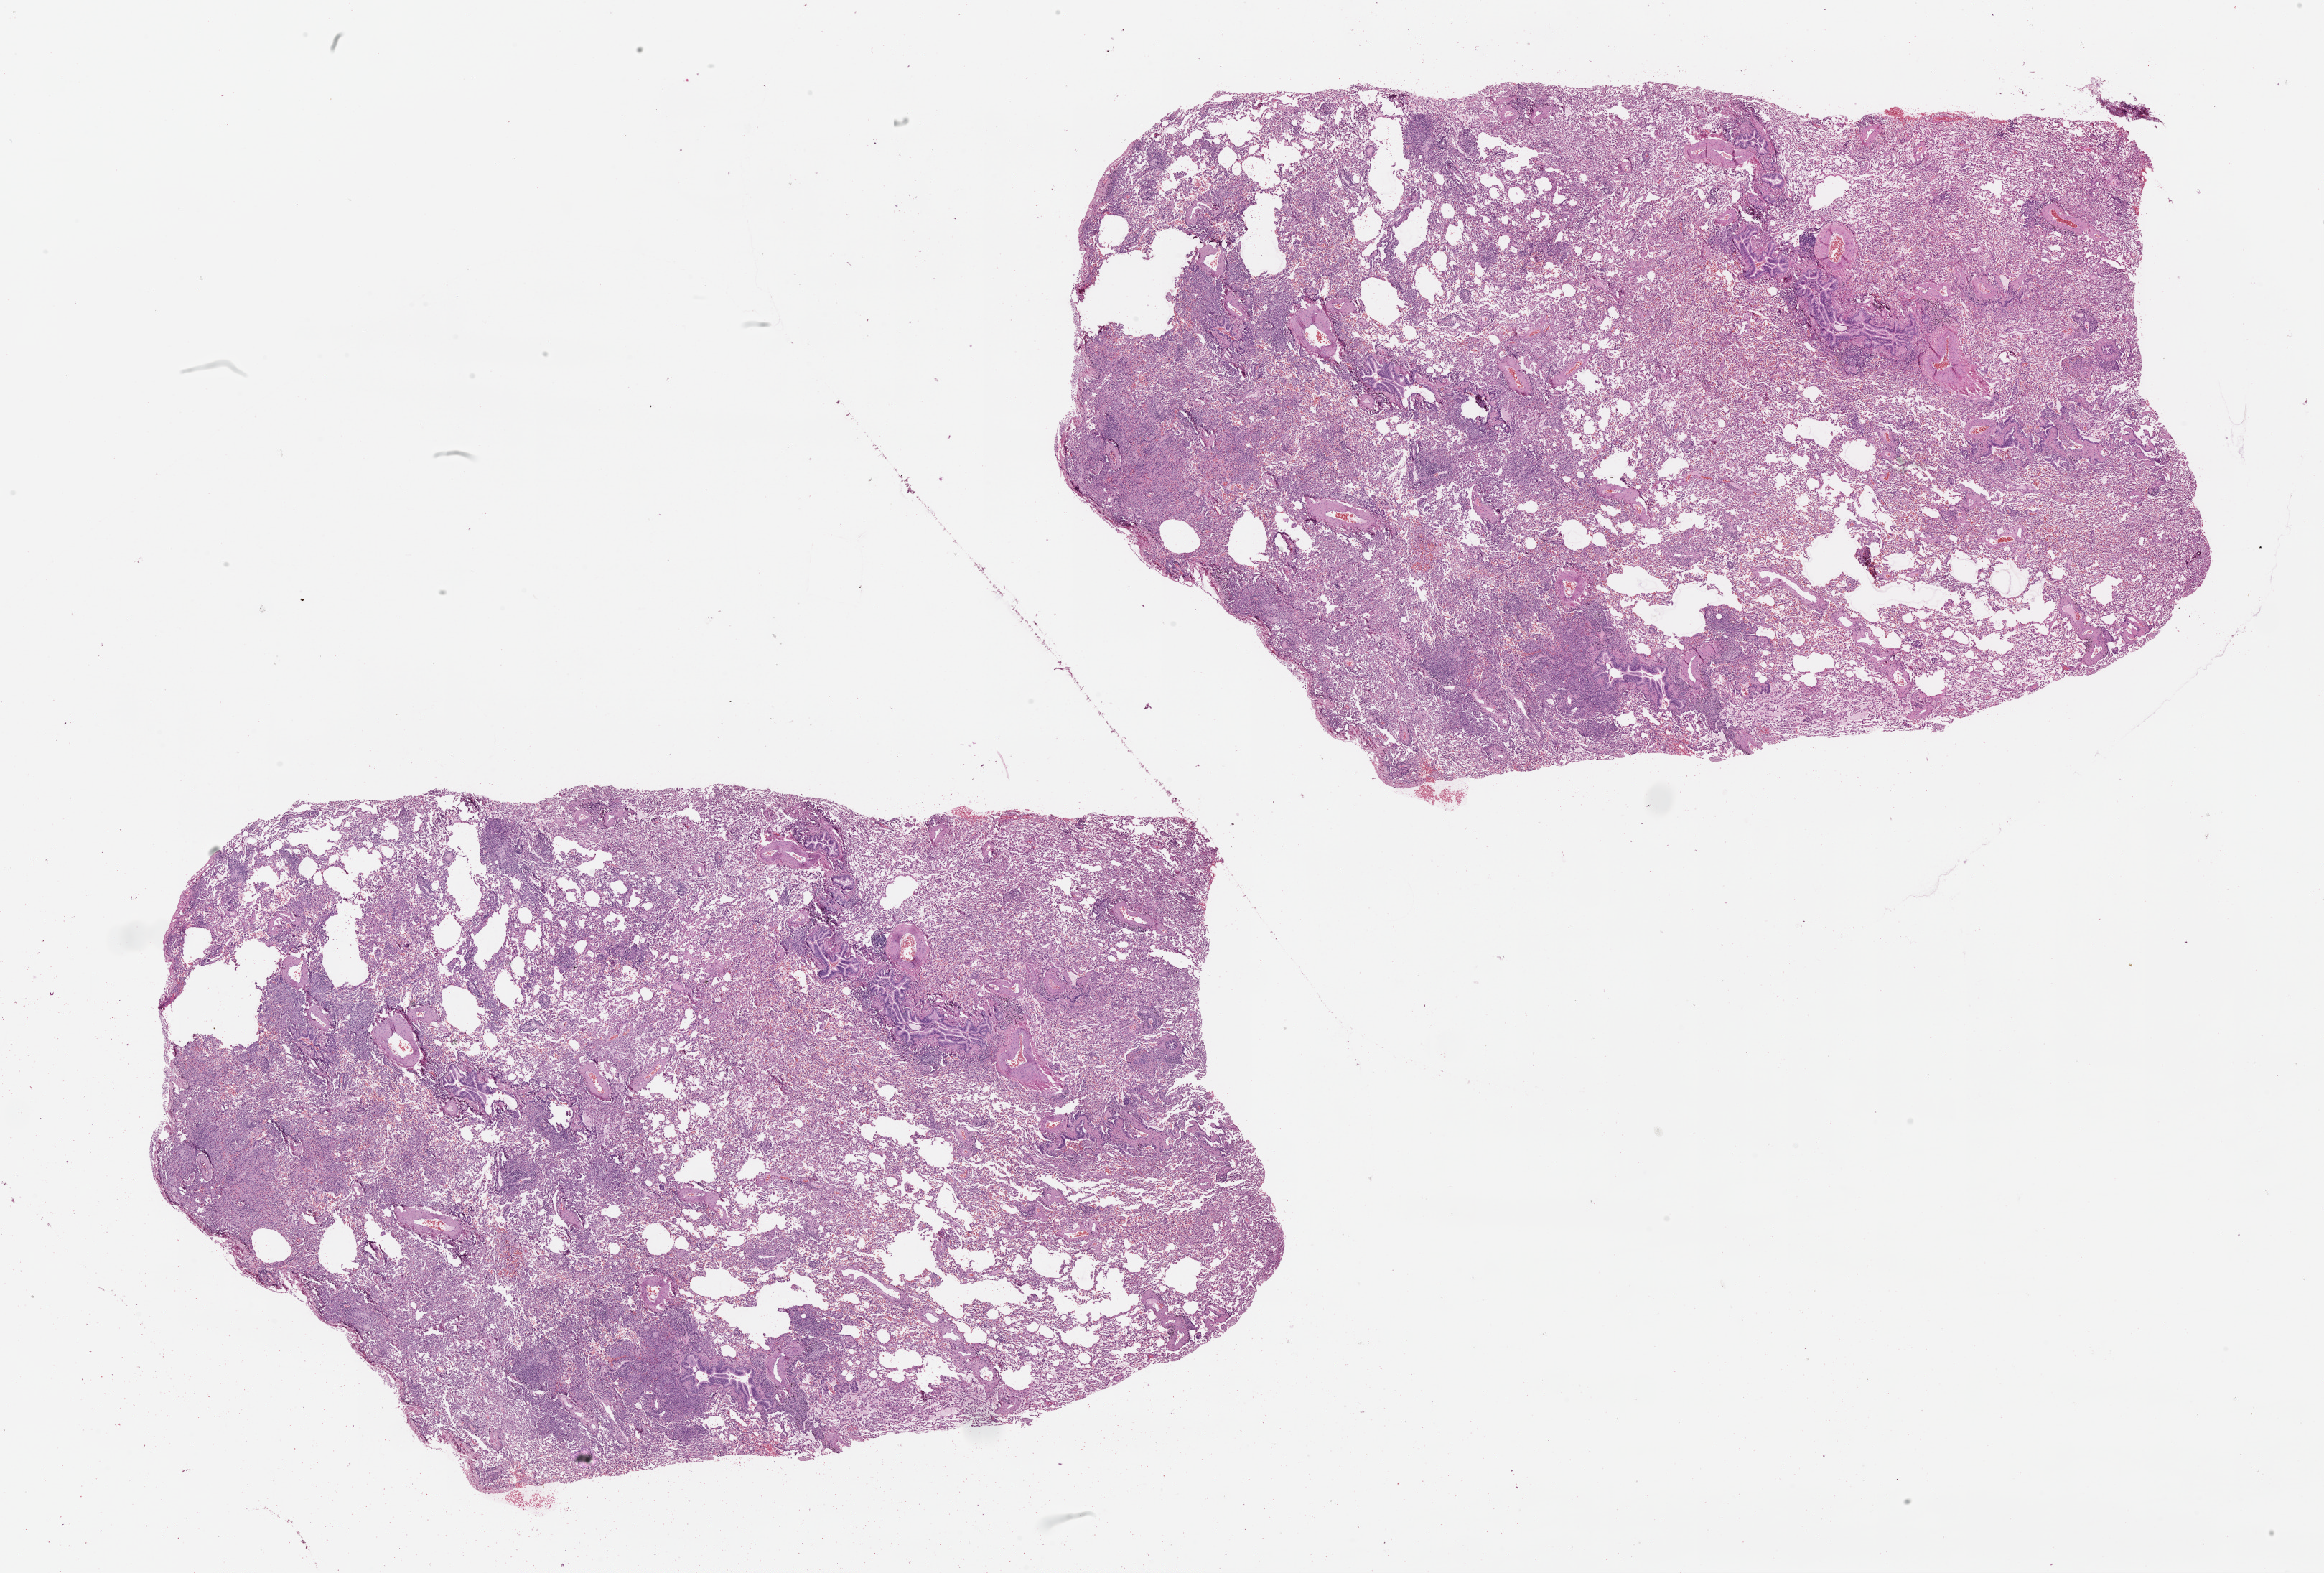
Whole-slide histology image, H&E-stained, shown as a low-resolution overview of the whole scanned area (about 26.1 x 17.6 mm); normal (non-tumour) tissue sample, lung. Patient: male, age 63 years.
This section: normal (non-tumour) tissue from the same patient. Patient diagnosis (cohort enrolment): squamous cell carcinoma (lung).